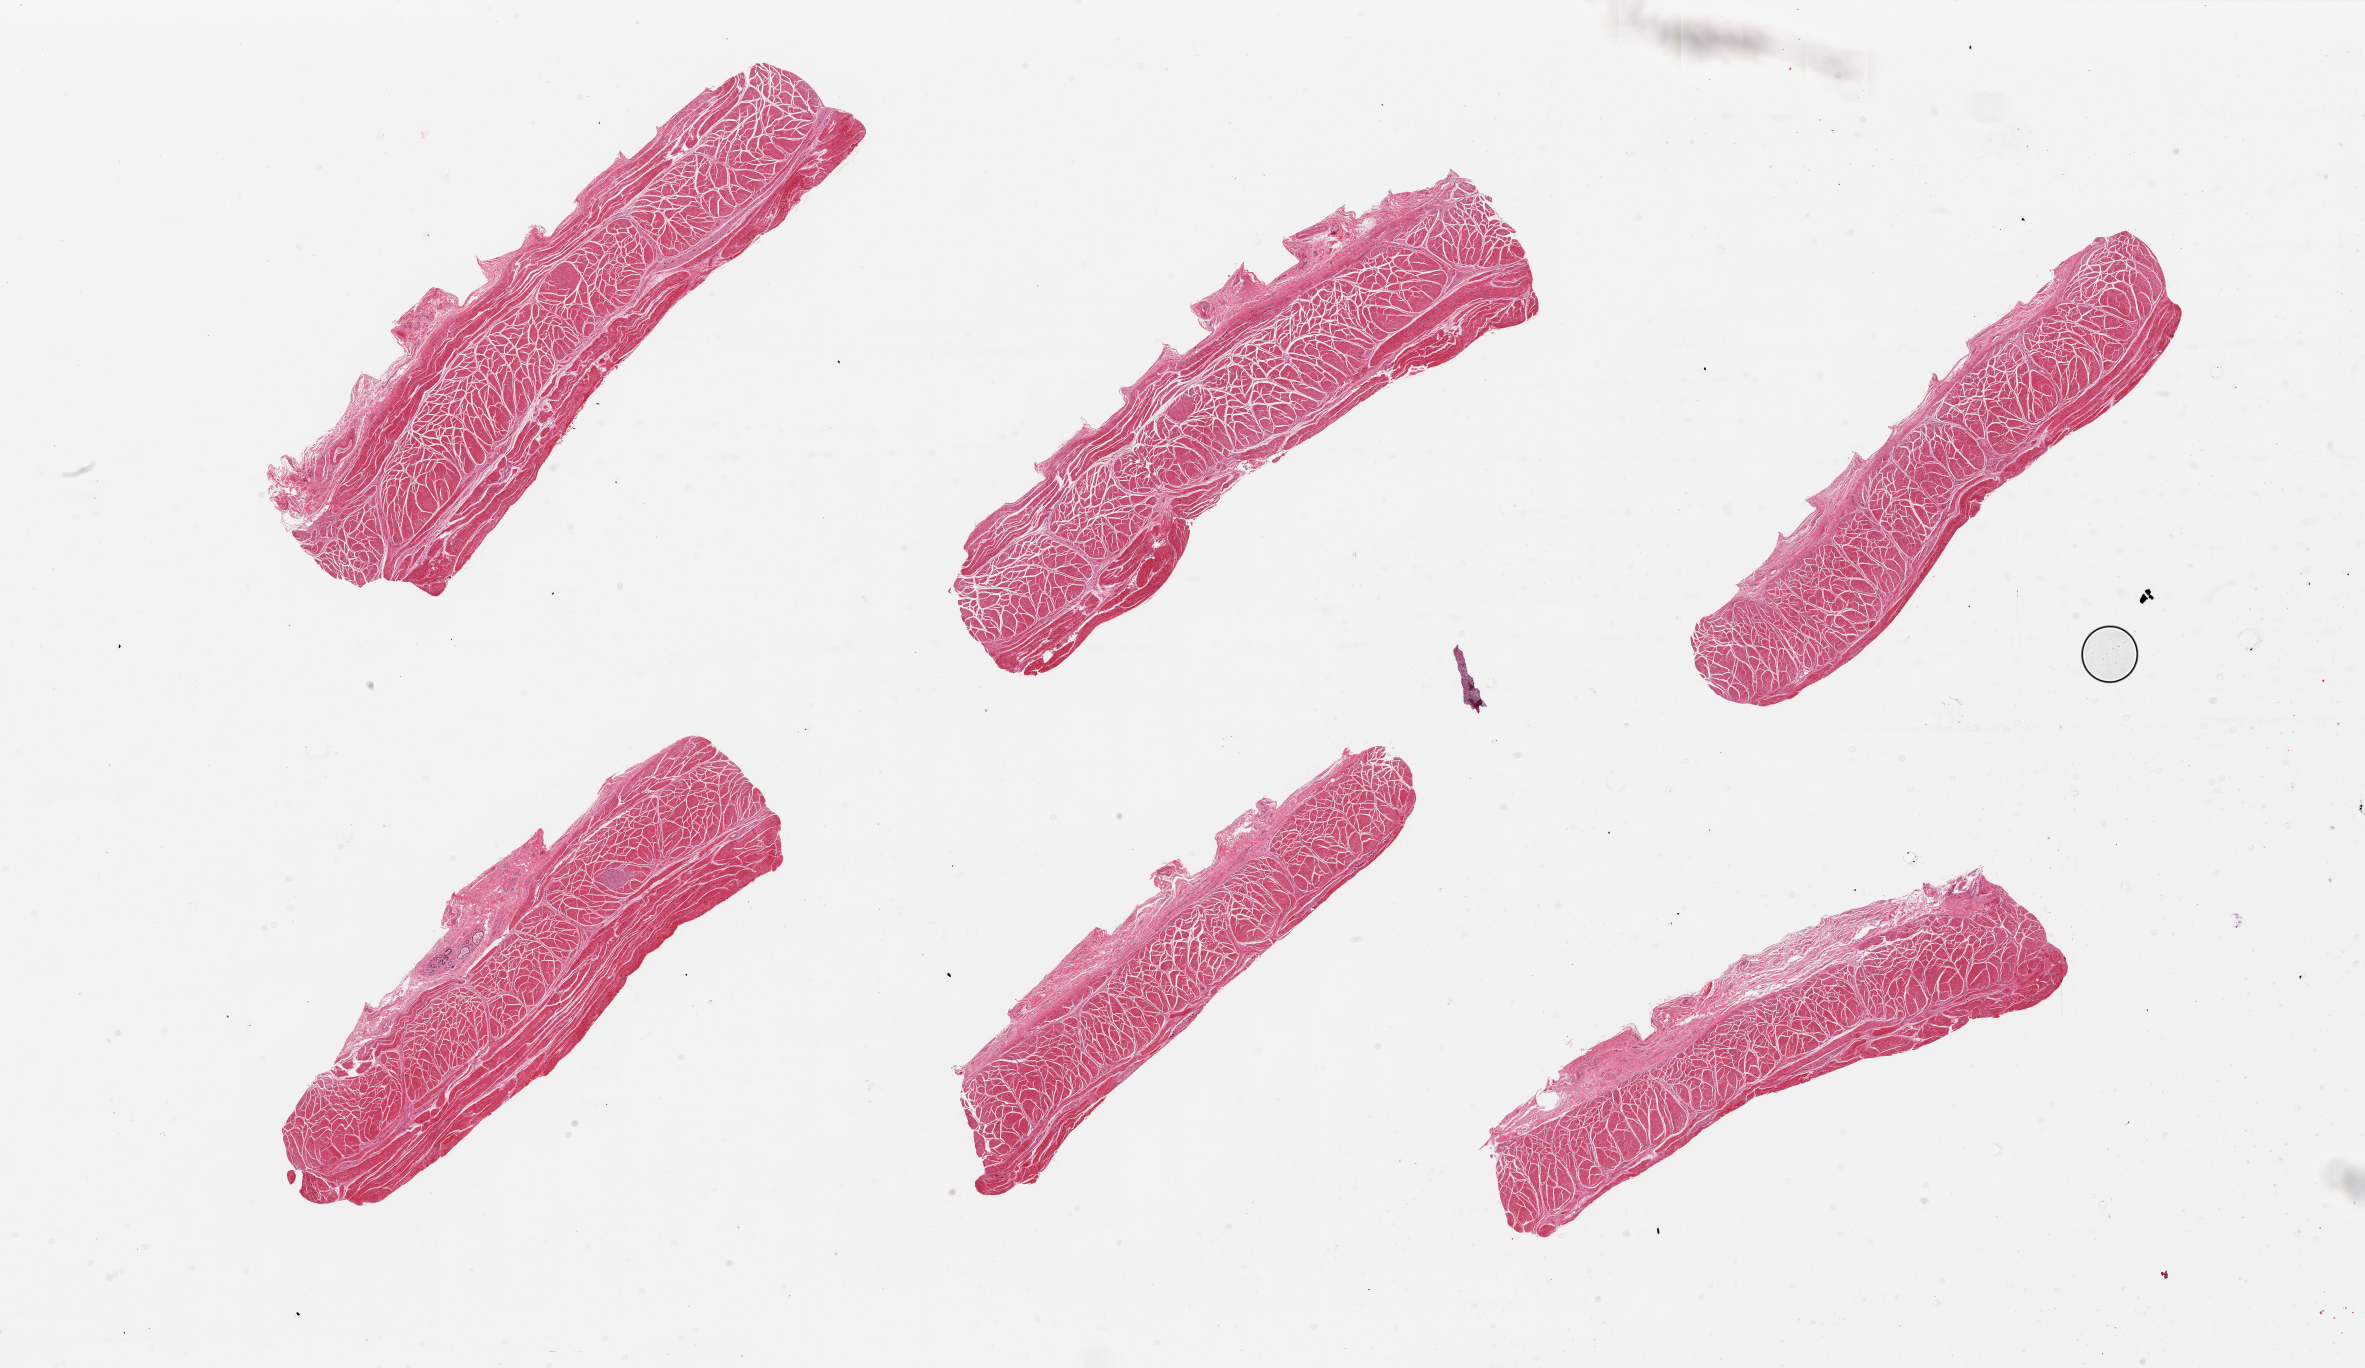
Hematoxylin and eosin (H&E) whole-slide image, brightfield, low-resolution overview of the scanned area, about 37.4 x 21.6 mm (from a 20x scan). PAXgene-fixed paraffin-embedded (PFPE) section. Section of esophageal muscle (target tissue). Donor tissue sample. Donor: male.
- reviewer comment on this tissue sample: 6 pieces; well dissected